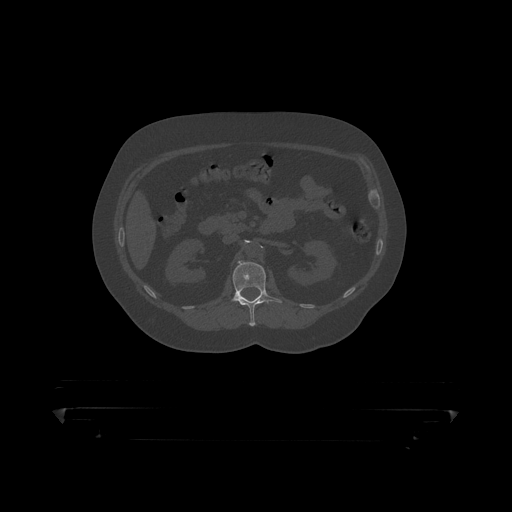
CT including the spine, one axial slice. Slice 143 of 390 in the series (ordered by position). Bone window (W 1800 / L 400 HU). 1.25 mm slice thickness. 512 × 512 image matrix, field of view 650 × 650 mm. Male patient, age 60 years. From the clinical record (not read from this slice): primary cancer: prostate.
Structures marked on this image (semi-automatically segmented with operator editing):
- L1 vertebra: box from (x=231, y=262) to (x=283, y=319) px